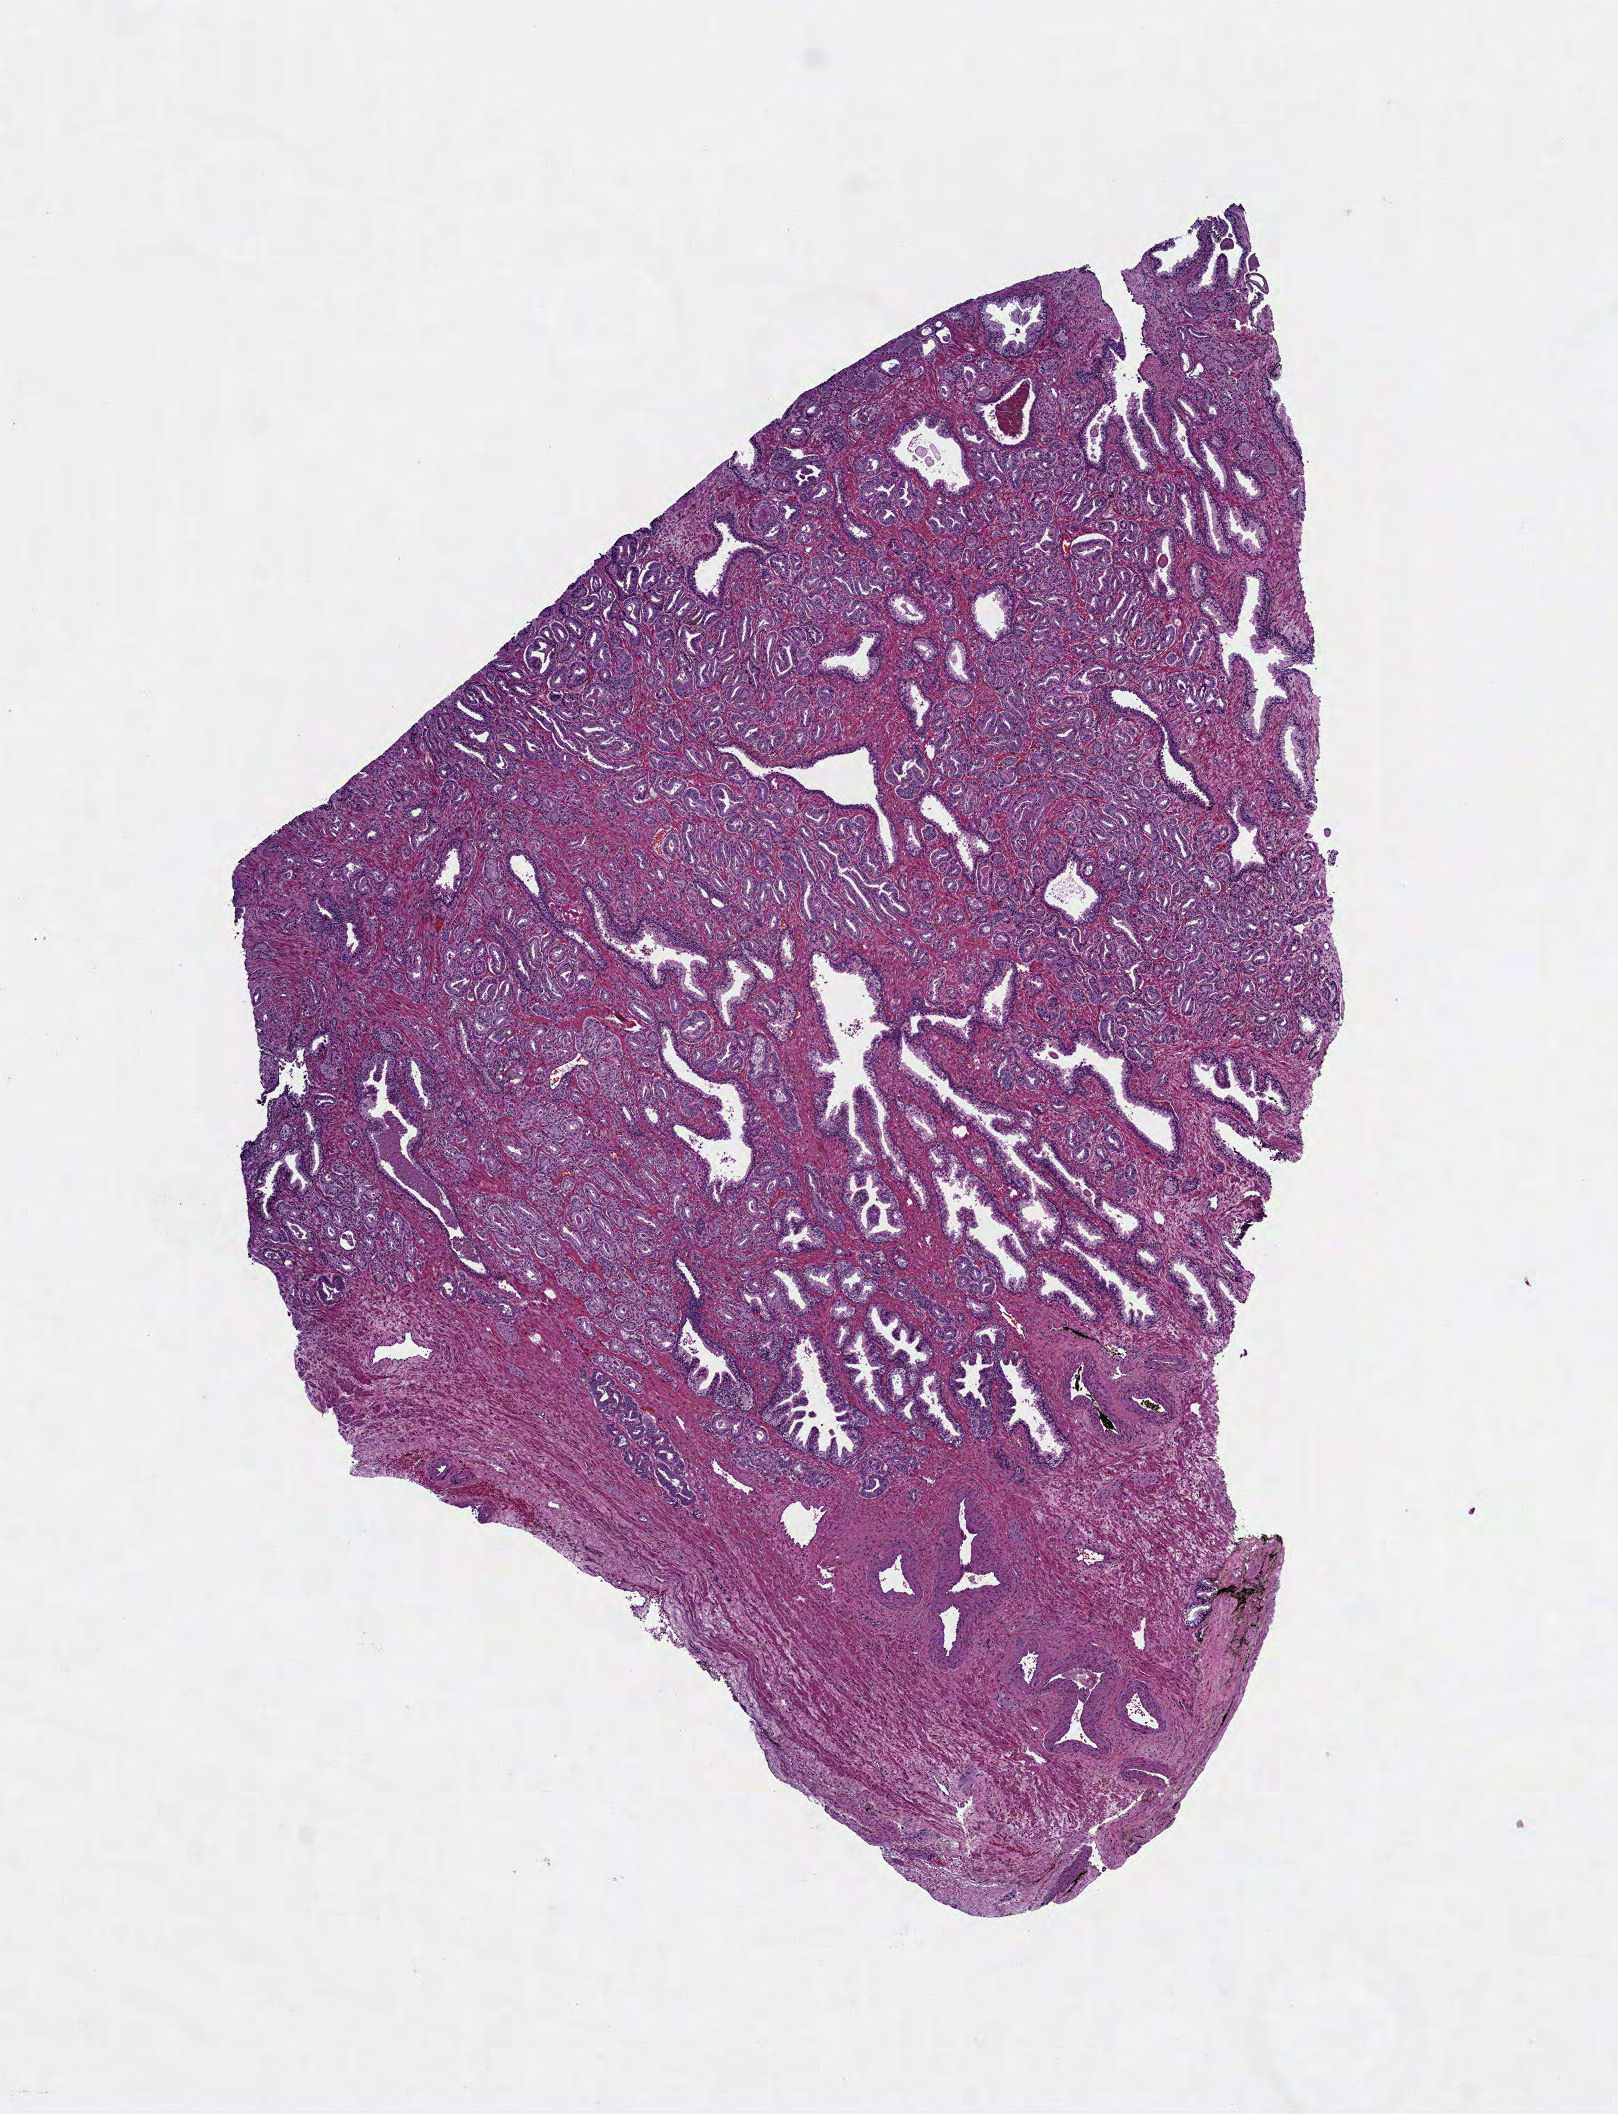
Hematoxylin and eosin (H&E) stained whole-slide image, shown as a low-resolution overview of the whole scanned area (about 6.5 x 8.5 mm), formalin-fixed paraffin-embedded (FFPE) diagnostic section, sample: primary tumour, prostate. Patient: male, age at initial diagnosis 60 years.
Diagnosis: Adenocarcinoma, NOS (prostate gland).